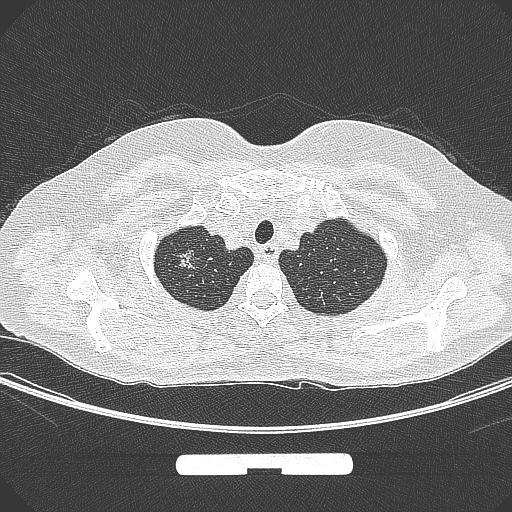
Chest CT, one axial slice. Slice 261 of 295 in the series (ordered by position). Lung window (W 1500 / L -600 HU). 1 mm slice thickness. 512 × 512 image matrix. Patient: female, 58 years. From the clinical record (not read from this slice): clinical TNM (as recorded): T1b N0 M0; histopathological grade: G2-3.
Annotated regions visible in this slice (bounding box drawn by a radiologist):
- lung tumour (recorded histology: adenocarcinoma): box from (x=172, y=235) to (x=200, y=277) px